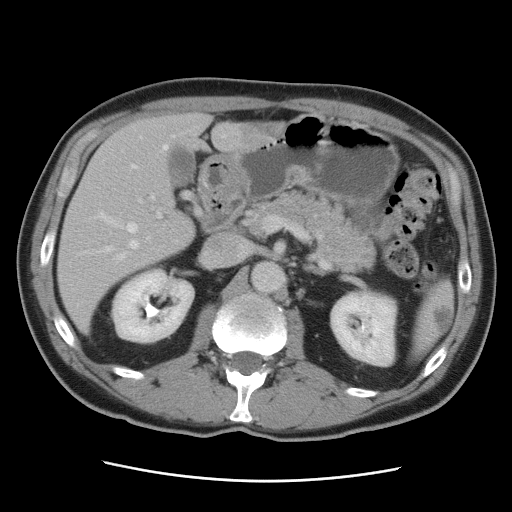
Contrast-enhanced abdominal CT, one axial slice. Position 48 of 89 along the scan axis. 120 kVp. Intravenous contrast given. Soft-tissue window (W 400 / L 40 HU). 5 mm slice thickness. 512 × 512 image matrix, field of view 366 × 366 mm. Male patient, age 59 years. From the clinical record (not read from this slice): diagnosis: colorectal cancer liver metastases, imaged before liver resection; multiple liver metastases: yes; largest metastasis: 0.6 cm; chemotherapy before resection: no.
Outlined on this slice (expert manual segmentation):
- hepatic veins: bounding box (x1, y1, x2, y2) in pixels: (82, 135, 226, 260)
- liver: (58, 114, 287, 336)
- planned liver remnant (the part of the liver to remain after resection): (71, 114, 211, 245)
- portal vein (with intrahepatic branches): (140, 196, 177, 242)
- liver metastasis: (242, 126, 283, 139)